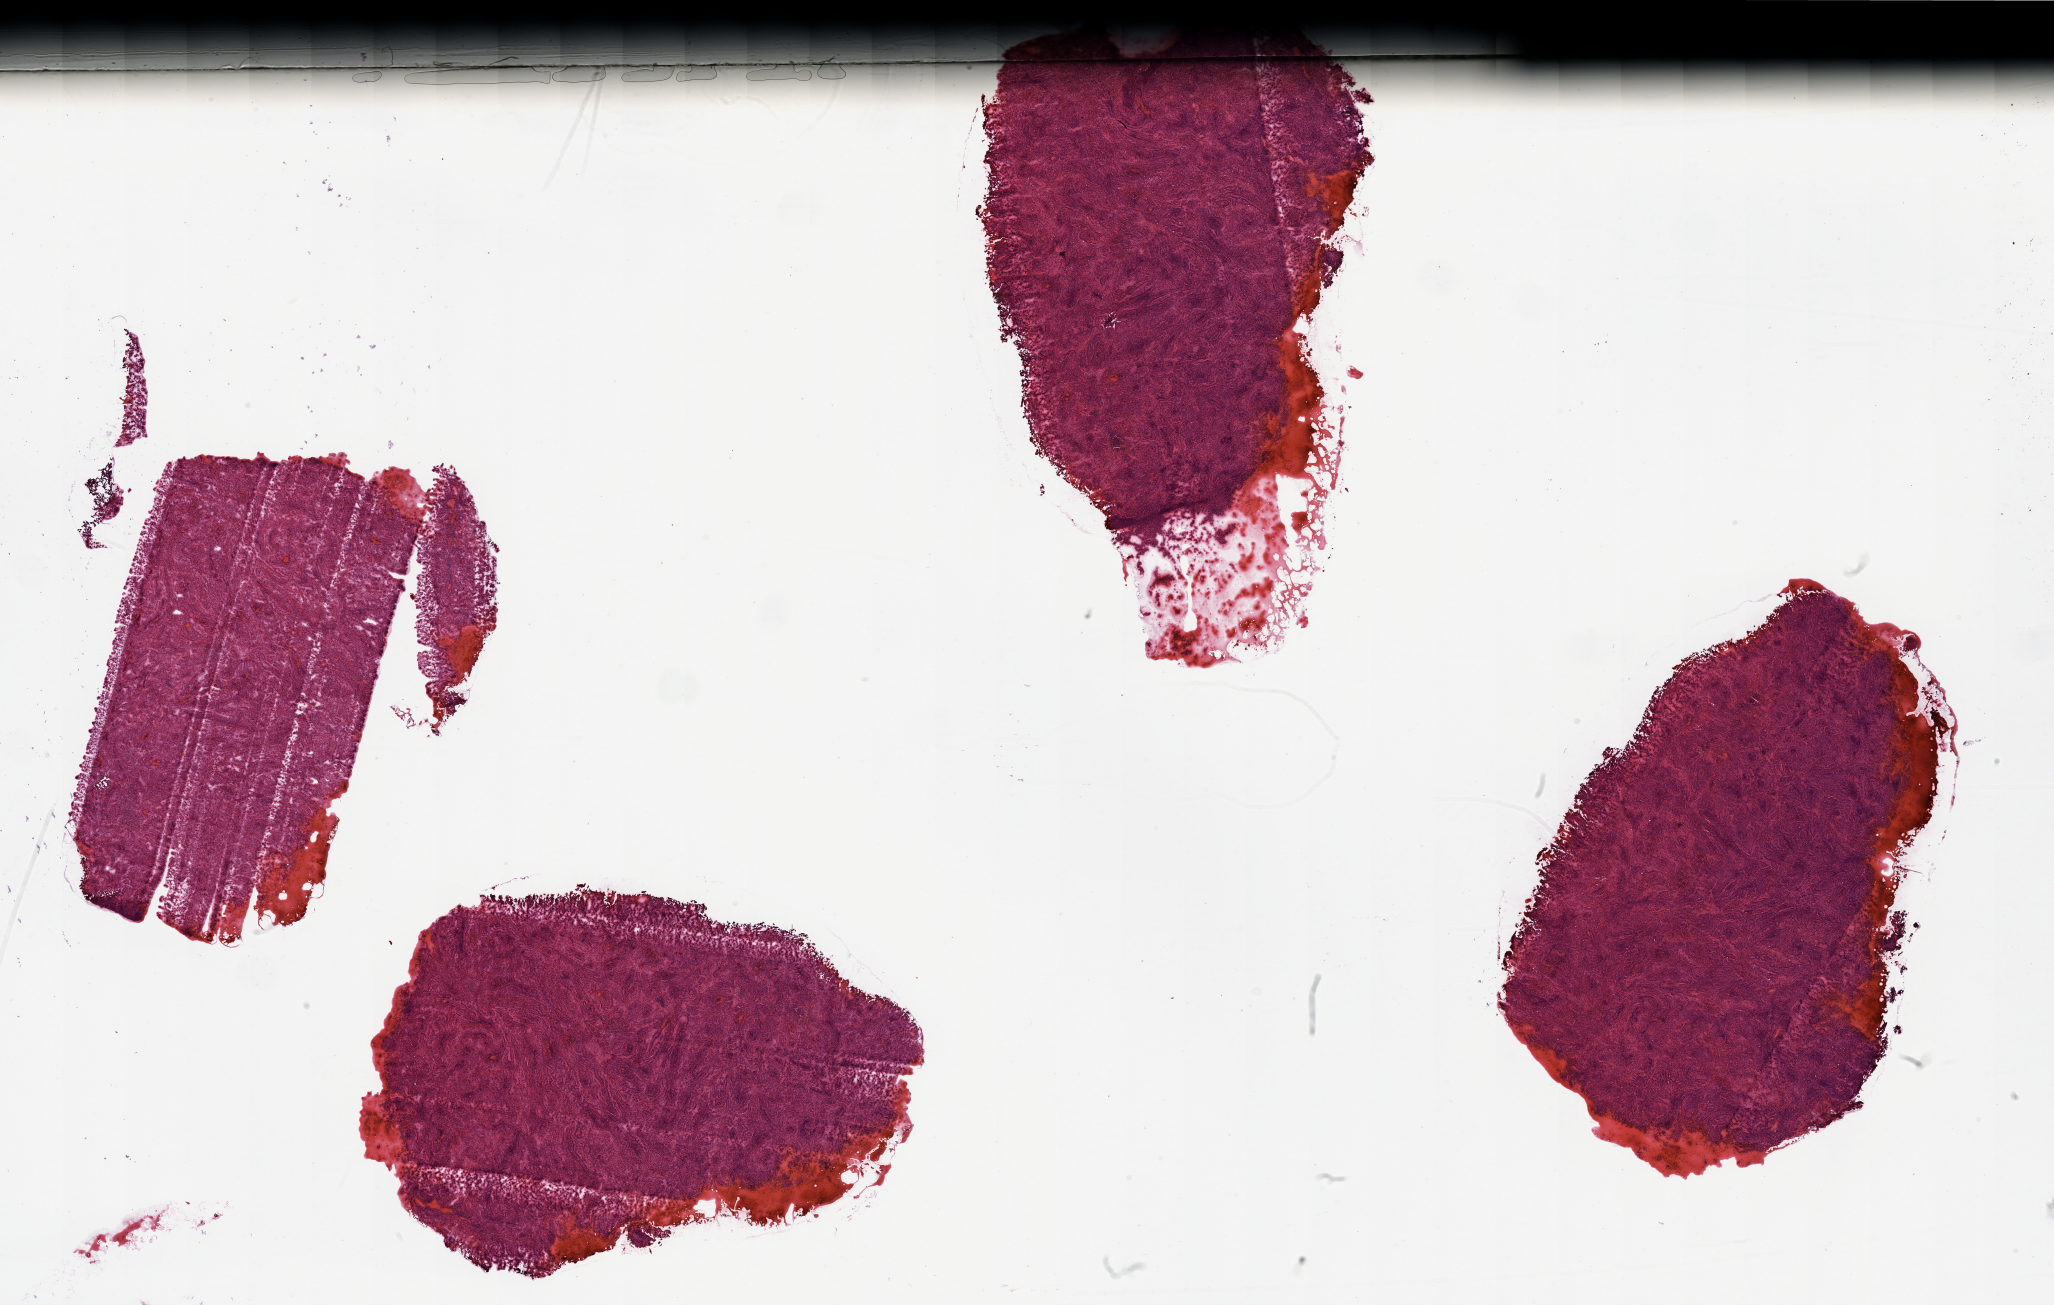
Digitized Hematoxylin and eosin (H&E) stained tissue section (whole slide) — whole scanned area (about 32.5 x 20.6 mm, acquisition: 20x scan) shown as a low-resolution overview. Tumour tissue sample, sampled site: lung. Patient: male, age 57 years. Histologic grade: GX (grade cannot be assessed). Slide review estimates, as recorded: tumour nuclei 80%, necrosis 10%.
Primary tumour site (as recorded): right lower lobe. Histologic diagnosis: Adenocarcinoma, NOS. AJCC pathologic stage: IIB.